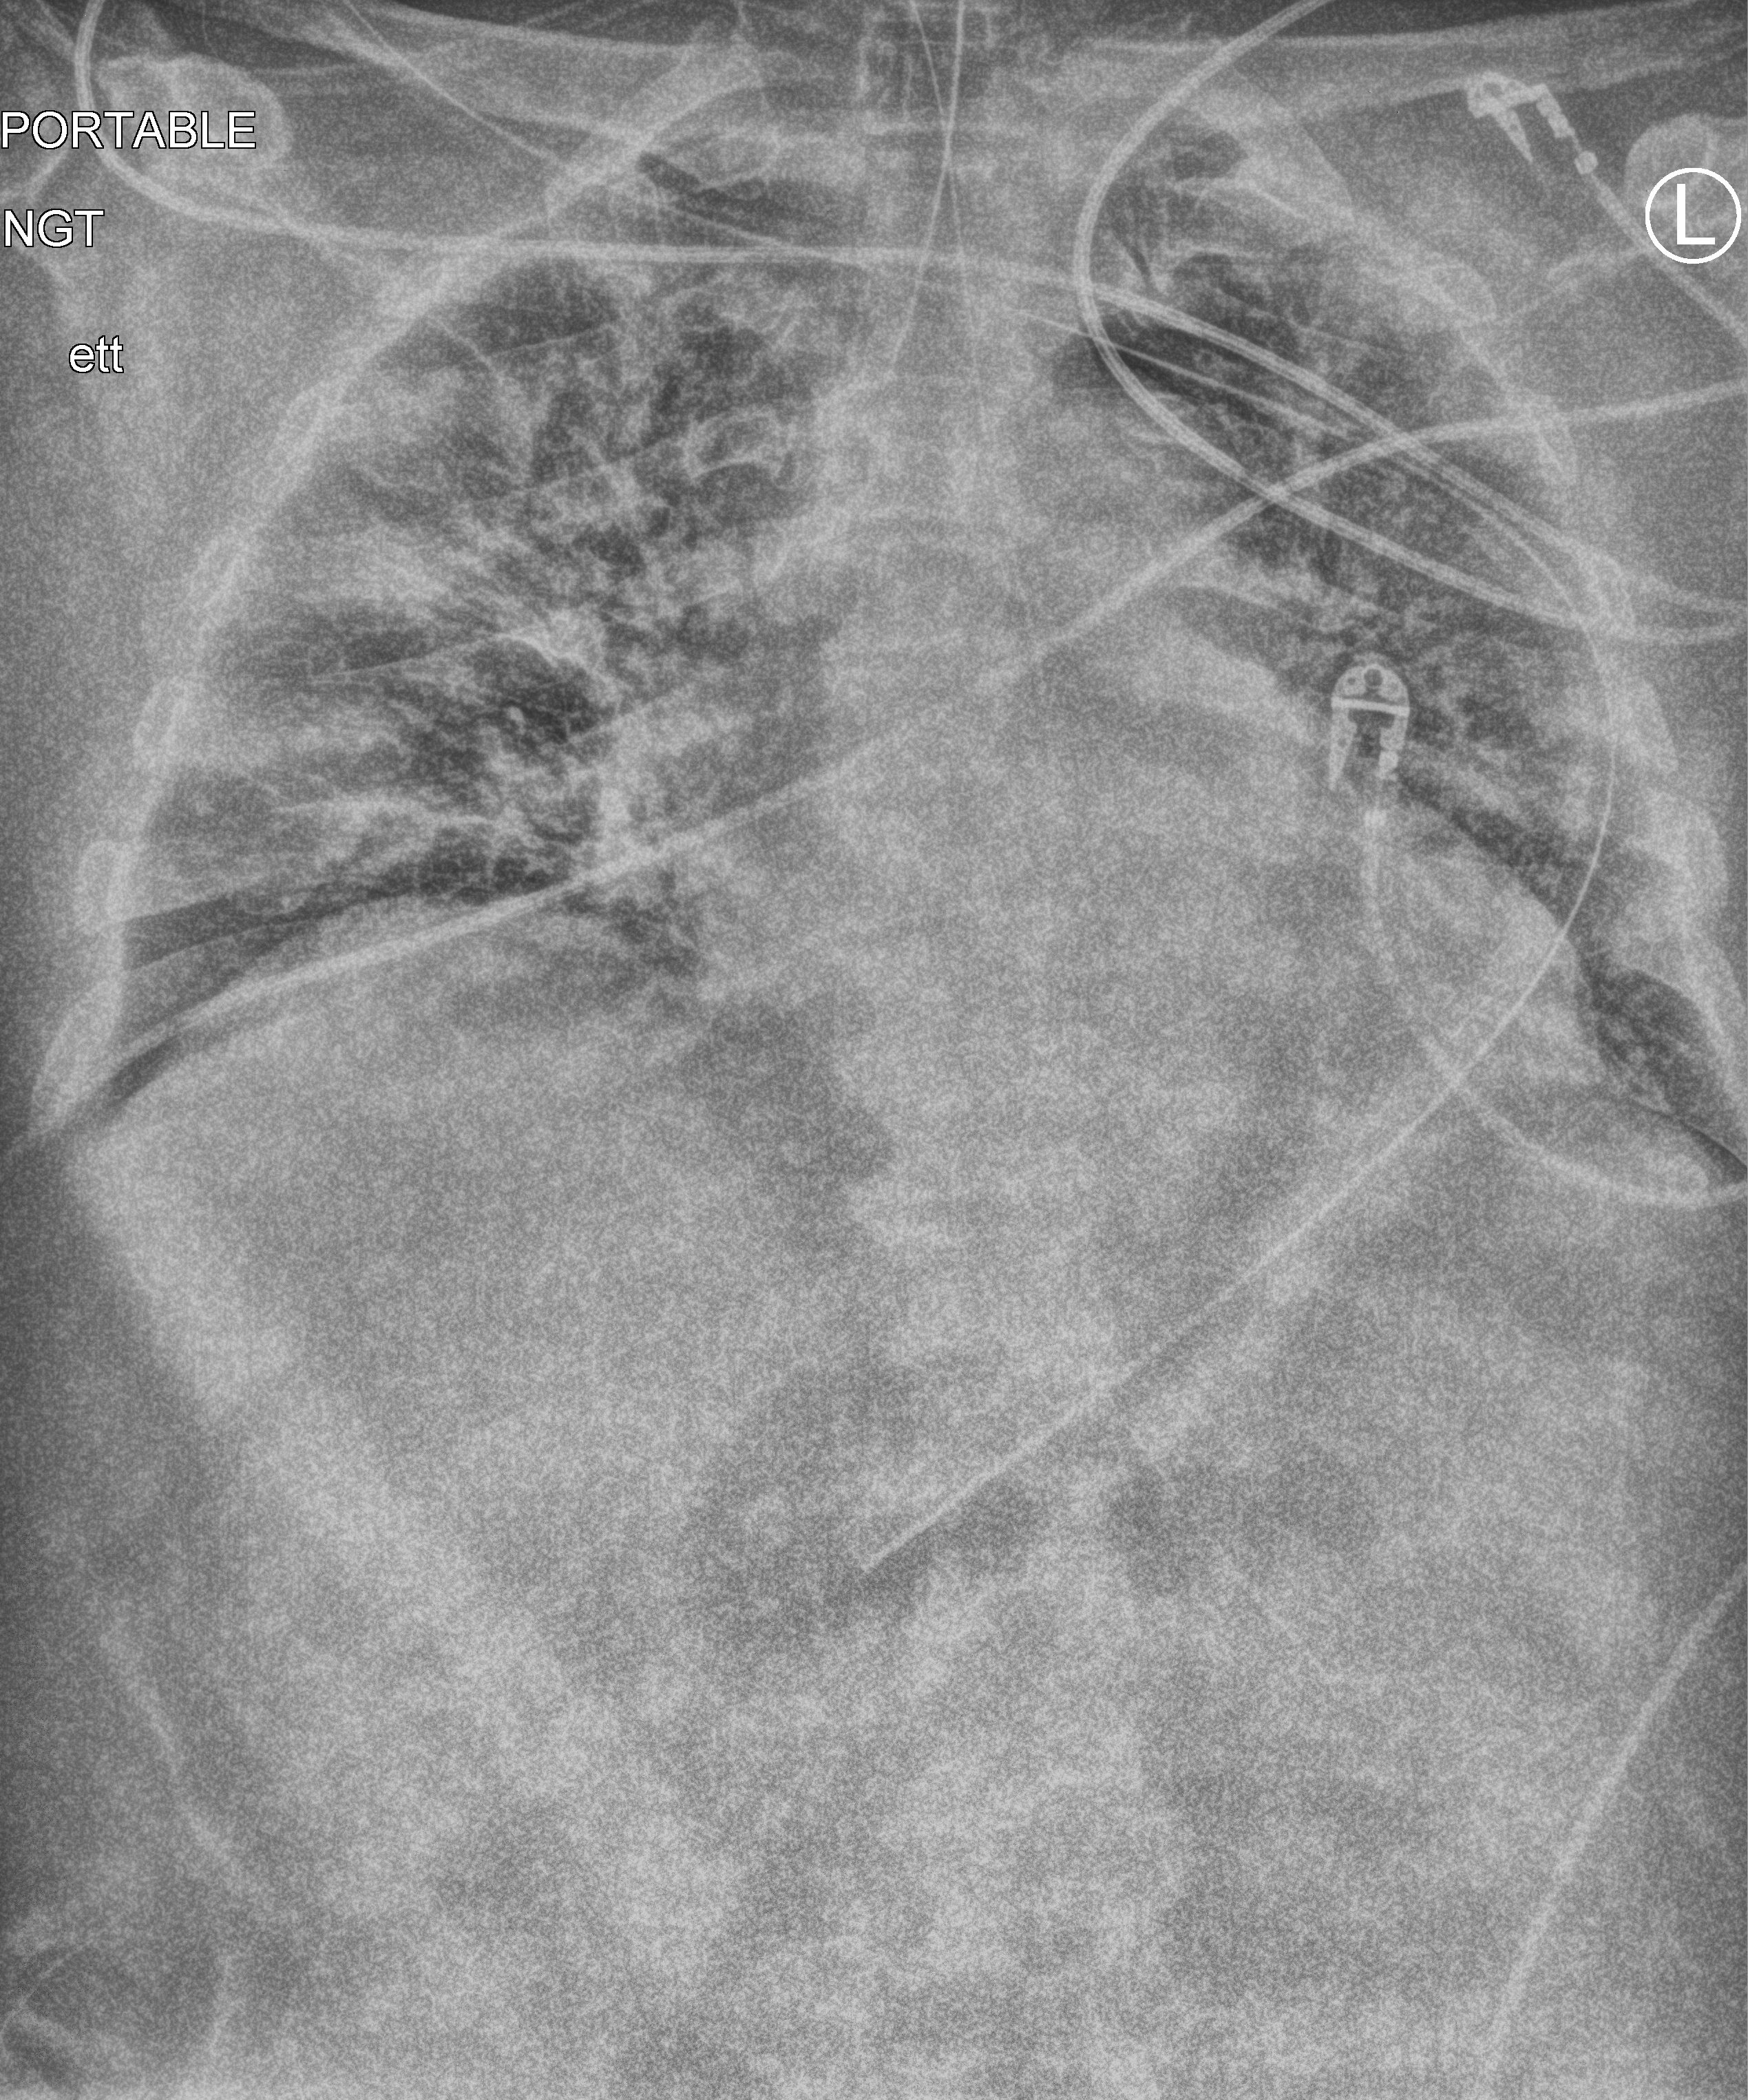
Portable chest radiograph; anteroposterior (AP) projection. Male patient hospitalised with COVID-19, age 60–74 years.
From the hospital-stay record, not from the radiograph (when in the stay this image was taken is not recorded): mechanically ventilated during this hospital stay: yes.